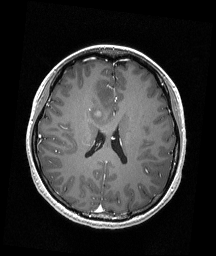
Brain MRI from a brain-tumour surgery series, one axial slice; position 78 of 192 along the scan axis; T1-weighted post-contrast; 216 × 256 image matrix, field of view 211 × 250 mm. From the clinical record (not read from this slice): histopathology: Astrocytoma; WHO grade: 4.
Outlined on this slice (expert manual segmentation):
- tumour: bounding box <97,112,100,114> (left, top, right, bottom; pixels)